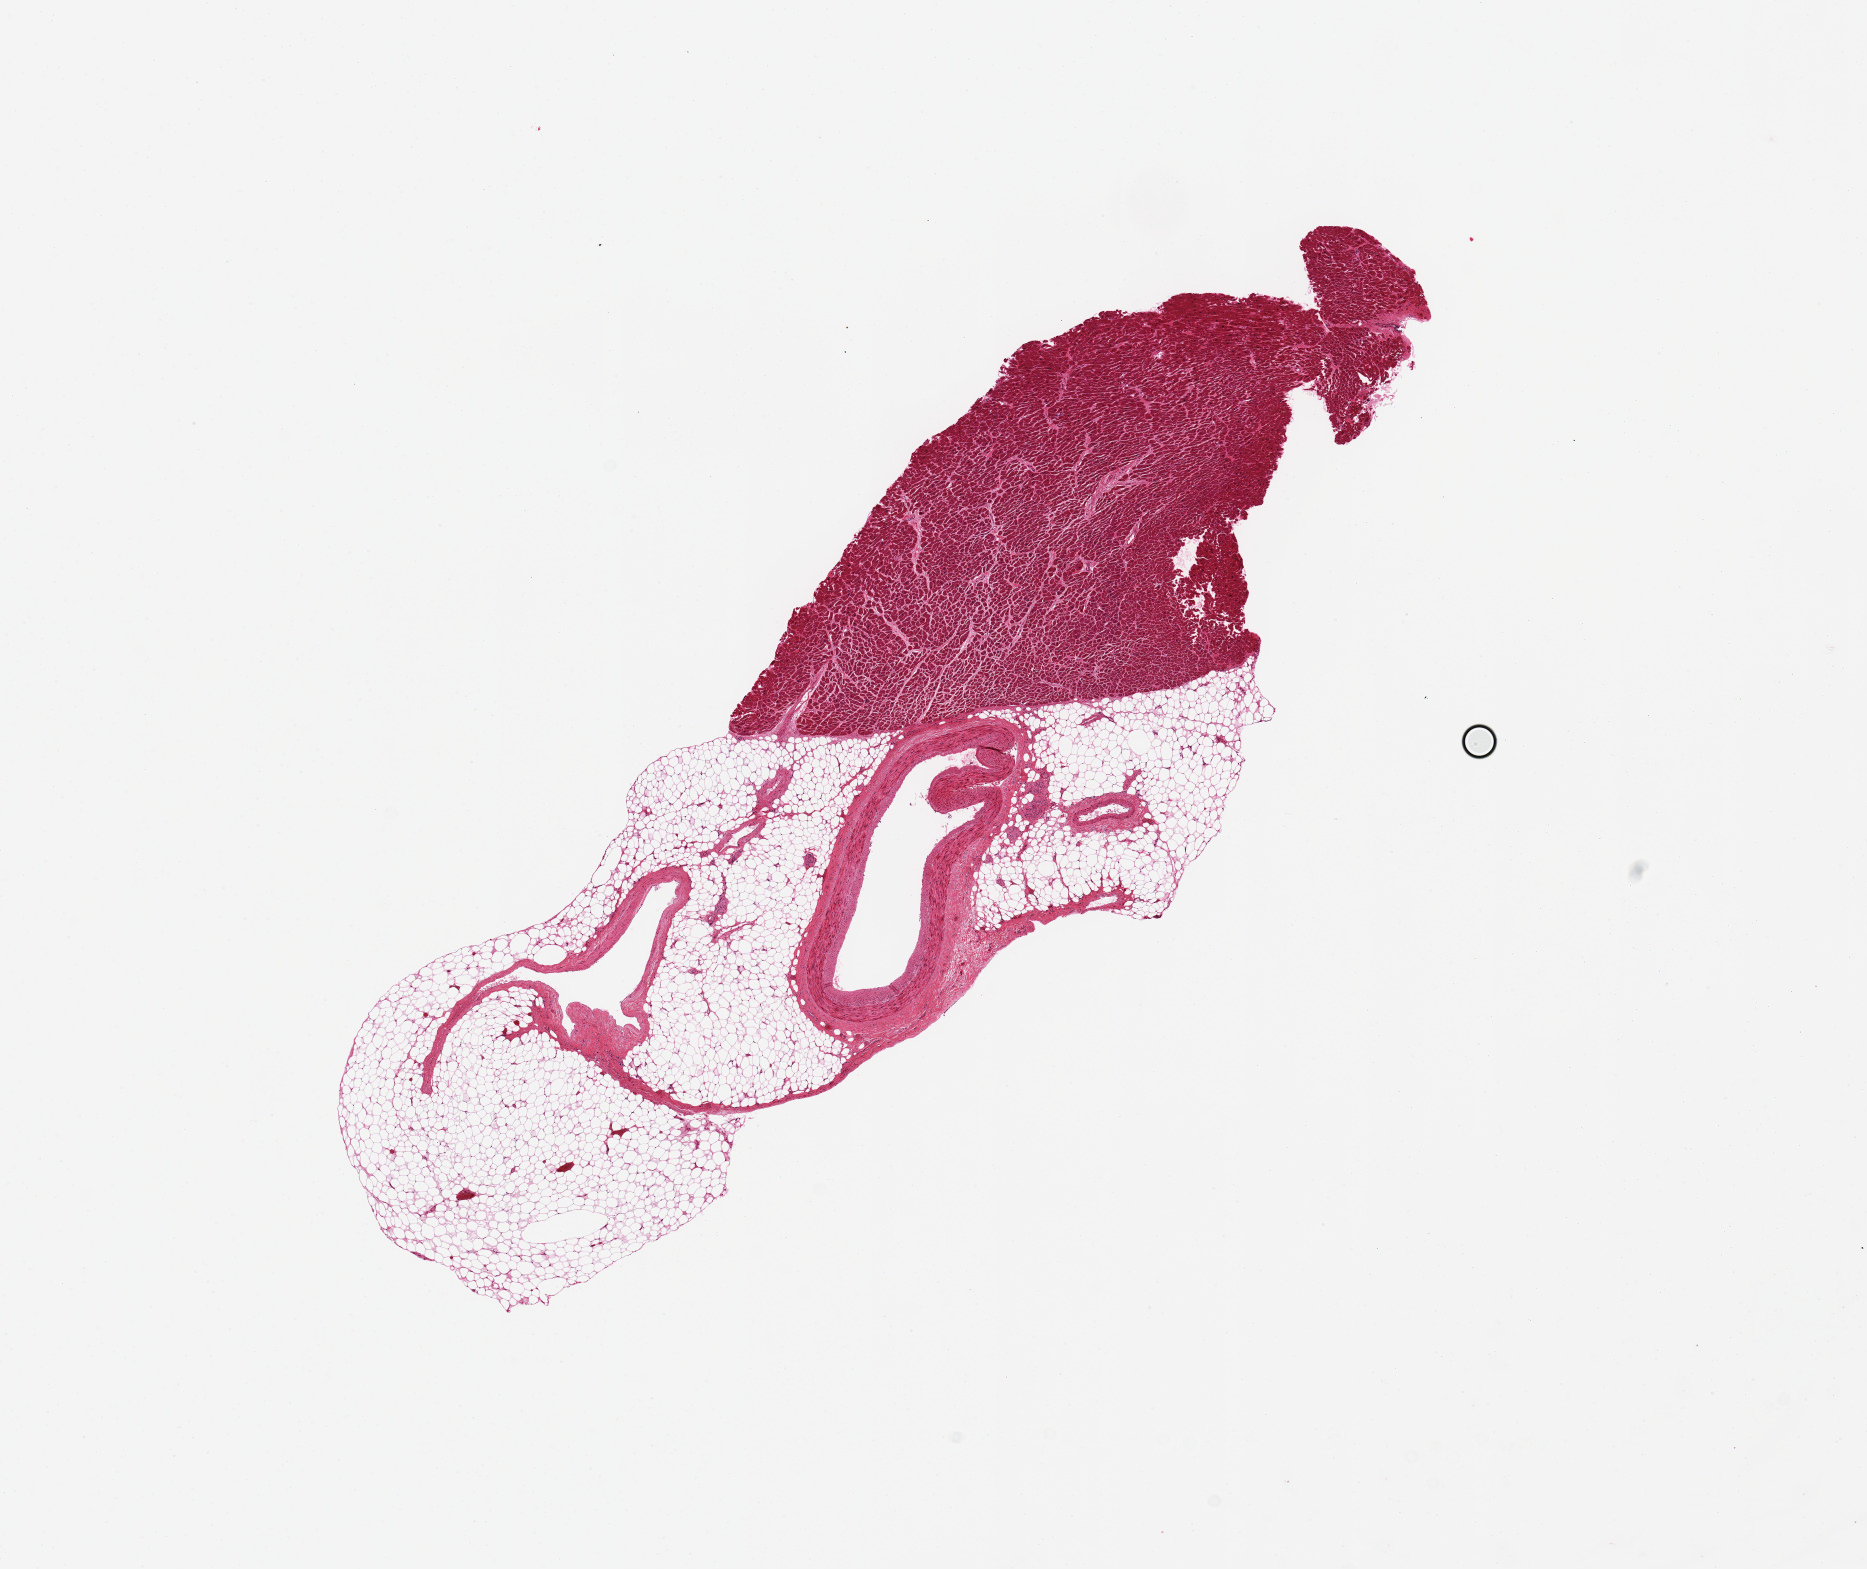
Hematoxylin and eosin (H&E) whole-slide image, a low-resolution overview of the entire scanned area, about 14.8 x 12.4 mm; PAXgene-fixed, paraffin-embedded tissue; section of coronary artery (target tissue); donor tissue sample. Donor: female.
Review note (as recorded): Less than 25% total tissue; remainder is fat and cardiac muscle (See Attachment A).